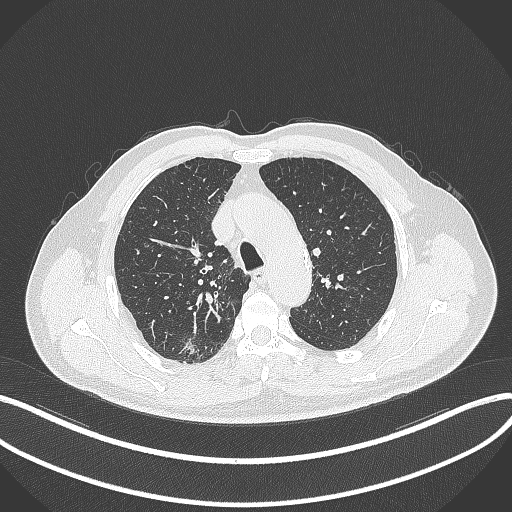
Chest CT, one axial slice; 120 kVp; lung window (W 1500 / L -600 HU); 1 mm slice thickness; 512 × 512 image matrix. Patient: male, 69 years. Case-level facts recorded for this patient, not image findings: clinical TNM (as recorded): T1b N0 M0; histopathological grade: G2-3.
Outlined on this slice (bounding box drawn by a radiologist):
- lung tumour (recorded histology: adenocarcinoma): bounding box <176,338,195,361> (left, top, right, bottom; pixels)